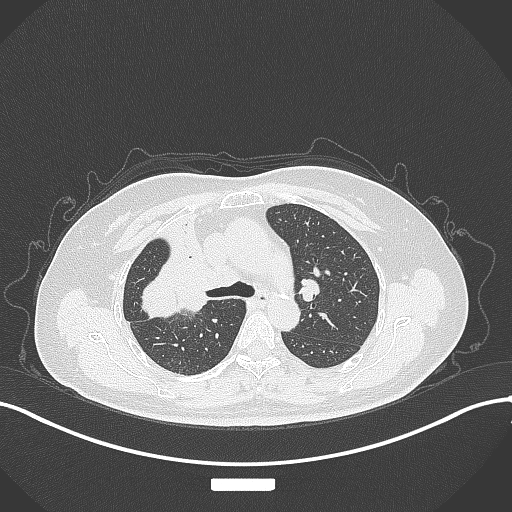
Chest CT, one axial slice. Position 212 of 309 along the scan axis. Reconstruction kernel B70f. 120 kVp. Lung window (W 1500 / L -600 HU). 1 mm slice thickness. 512 × 512 image matrix, field of view 400 × 400 mm. Patient: female, 60 years. From the clinical record (not read from this slice): clinical TNM (as recorded): T3 N1 M1.
Structures marked on this image (bounding box drawn by a radiologist):
- lung tumour (recorded histology: adenocarcinoma): bounding box <130,249,204,320> (left, top, right, bottom; pixels)